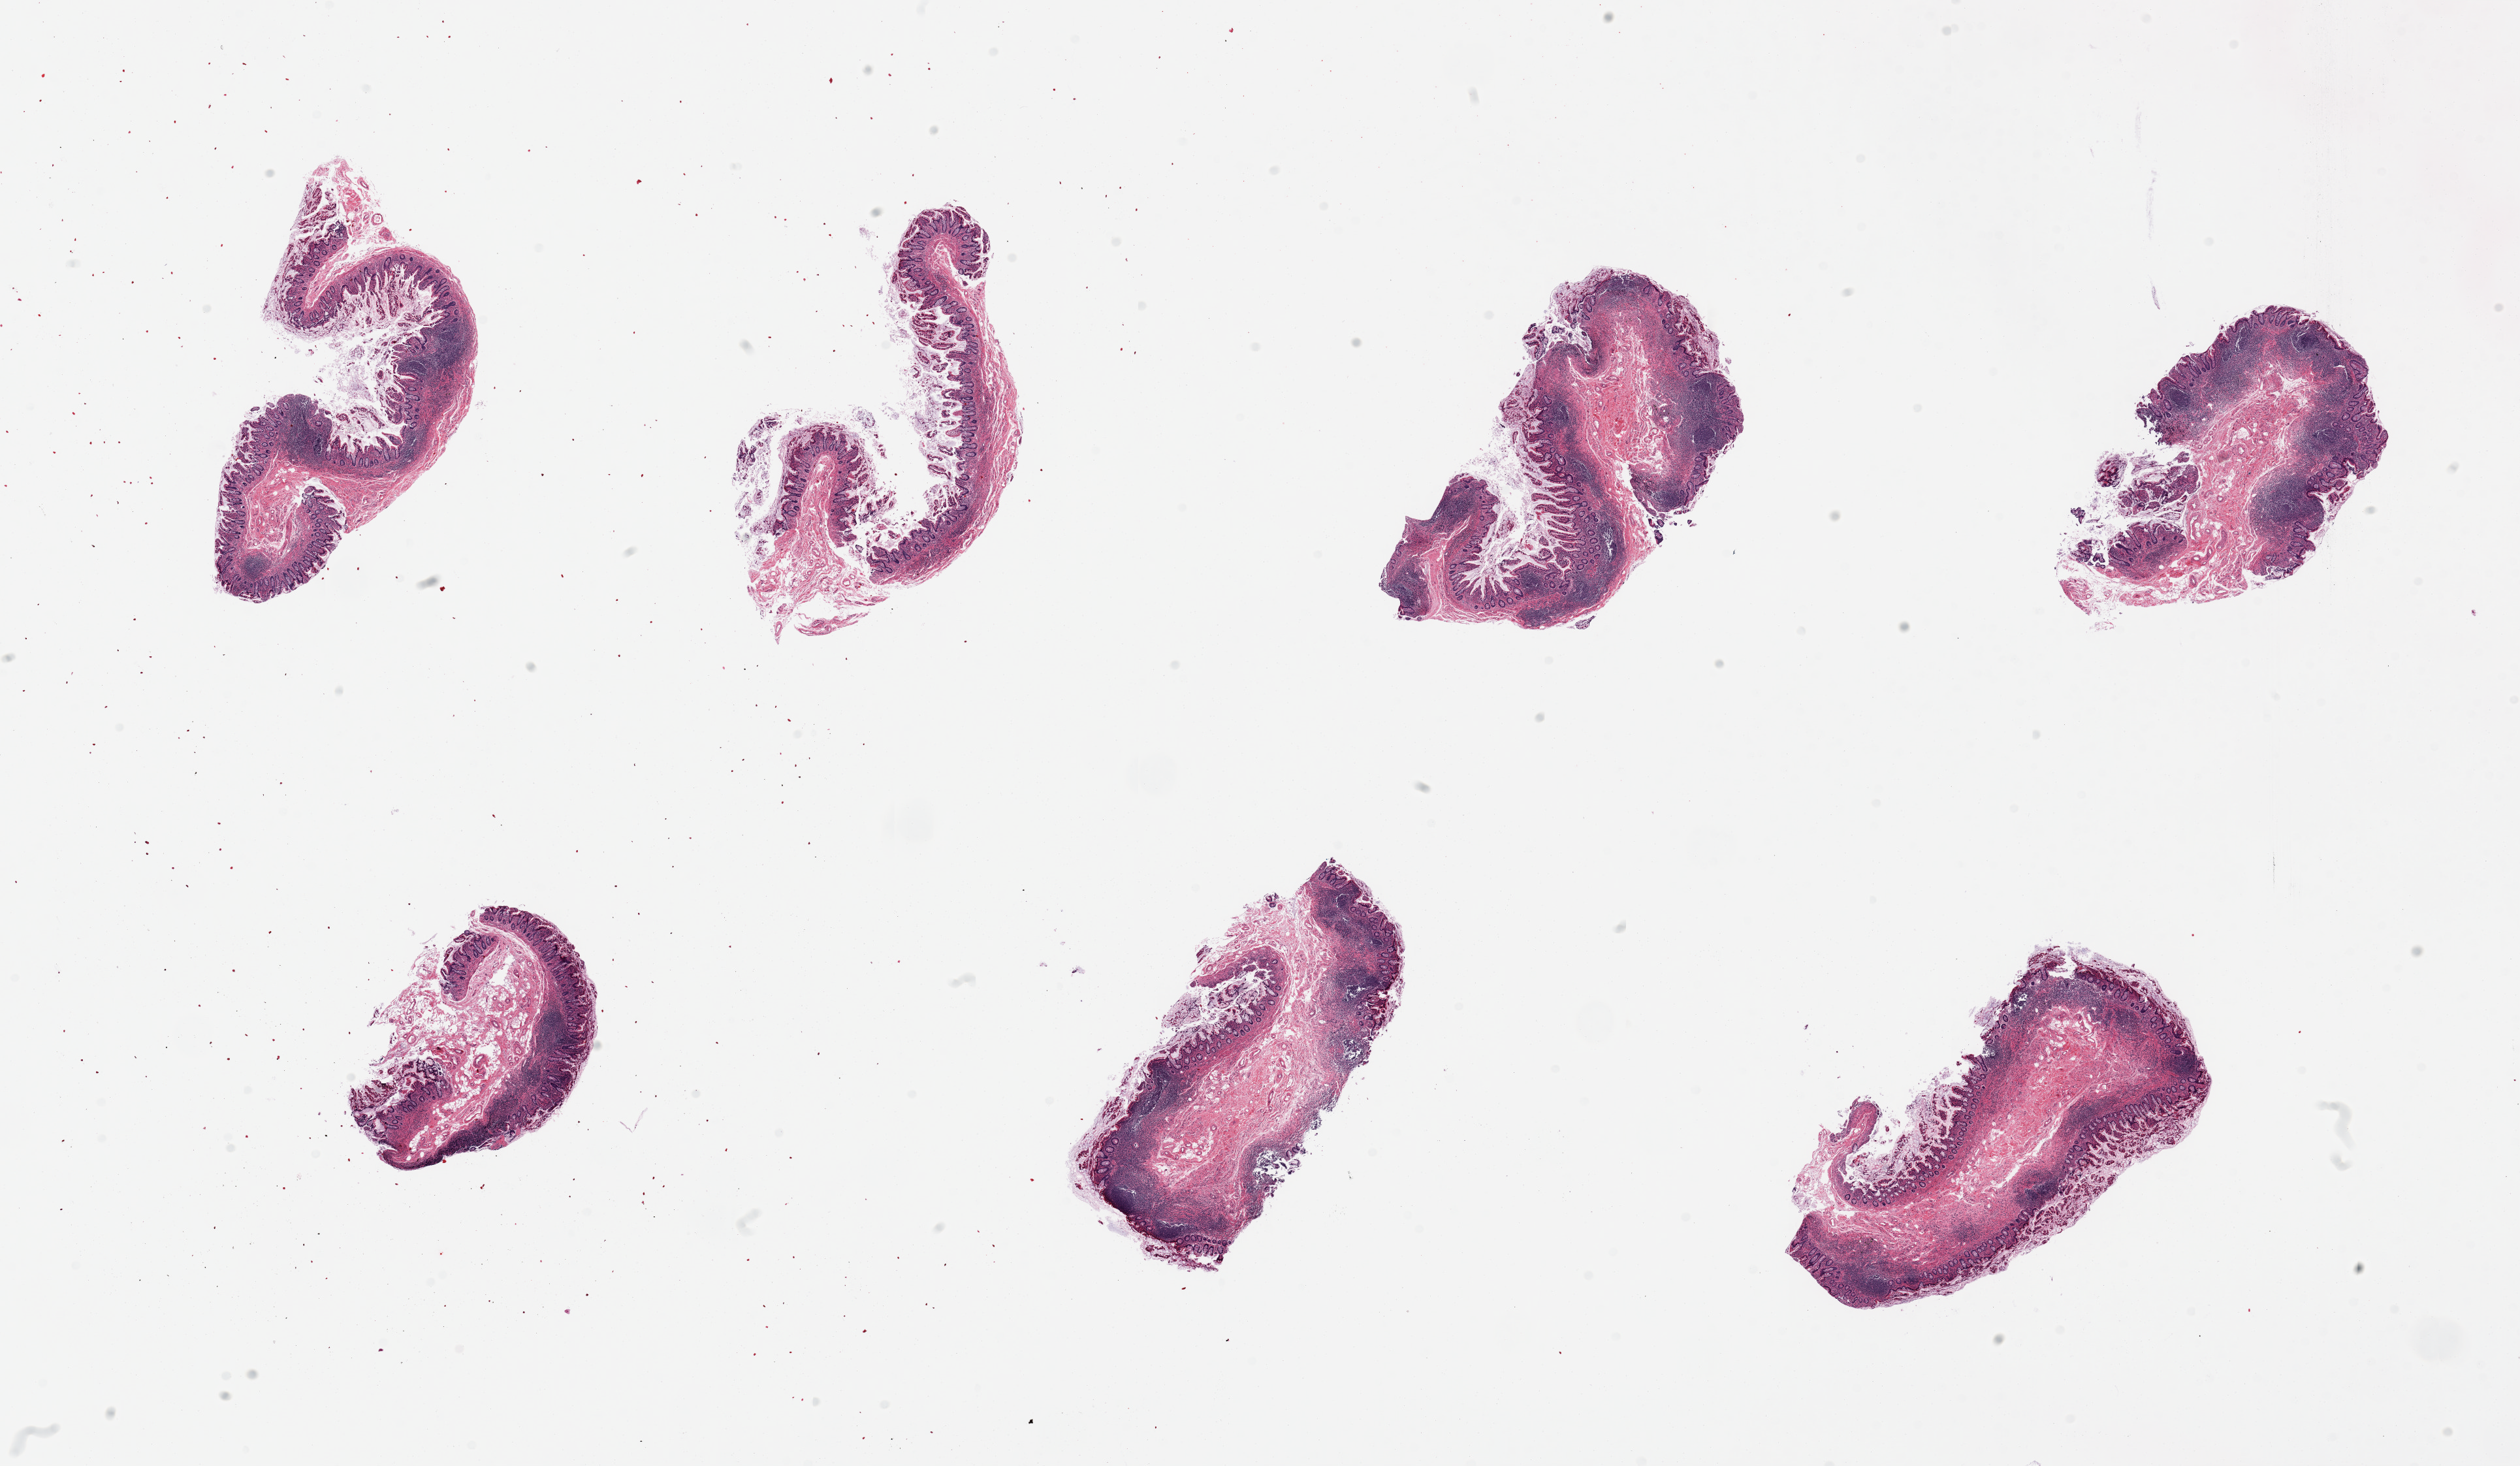
Whole-slide image, hematoxylin and eosin (H&E) stain, brightfield, low-resolution overview of the scanned area, about 30.5 x 17.8 mm. PAXgene-fixed, paraffin-embedded tissue. Section of ileum (target tissue). Donor tissue sample. Donor sex: male.
Review note (as recorded): 7 pieces, mucosa and submucosa only, several pieces with good lymphoid component.